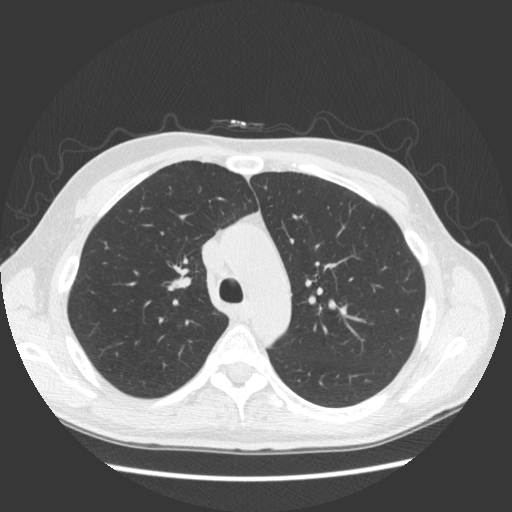
Axial slice from a low-dose chest CT screening exam, second annual screen, lung window (W 1500 / L -600 HU), 120 kVp, slice 53 of 163 in the series. Male, age 57 years at enrolment. Former smoker at enrolment.
Expert reader's lesion annotation, bounding box (x1, y1, x2, y2) in pixels: (152, 246, 204, 302). The screening reader recorded 3 non-calcified nodules or masses ≥4 mm on this exam (right middle lobe, right middle lobe, right middle lobe); which of them this box marks is not recorded. Participant outcome: lung cancer diagnosed 264 days after this screen — adenocarcinoma, NOS, right upper lobe, poorly differentiated (G3), stage IB (AJCC 6th edition), 25 mm at pathology.